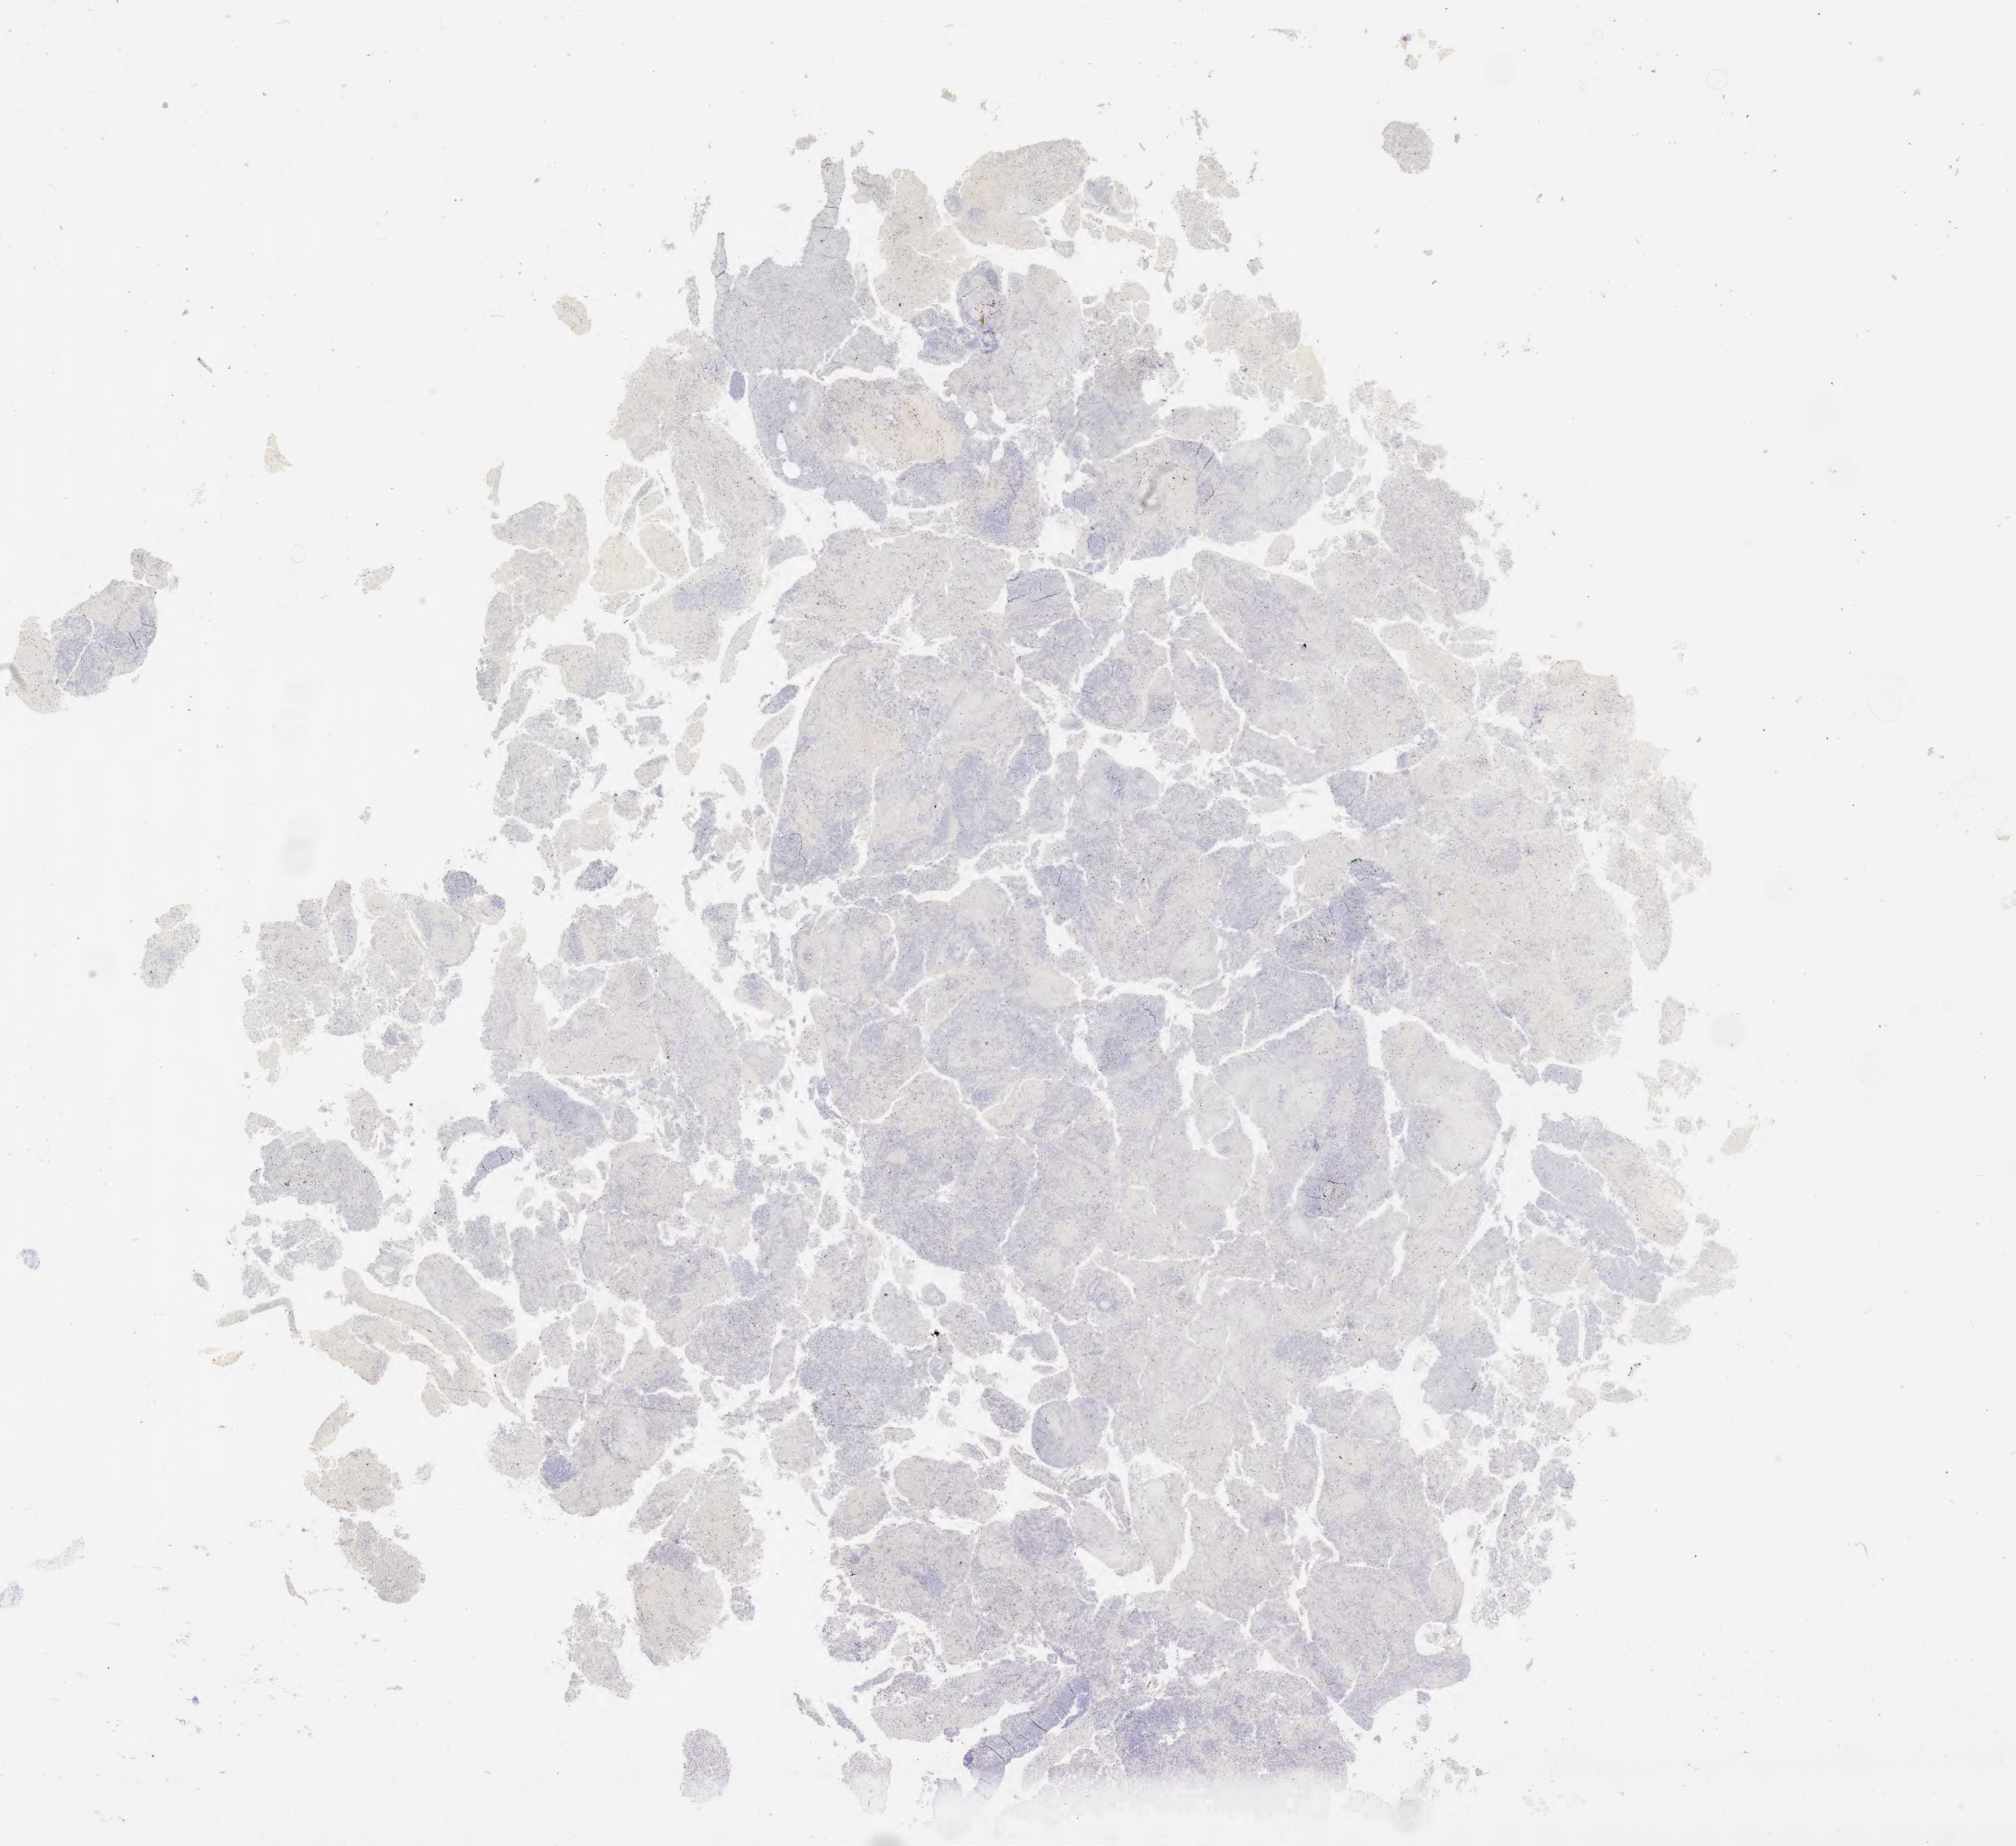
Immunohistochemistry (IHC) whole-slide image stained for CD3 — low-resolution overview of the scanned area, about 20.6 x 18.9 mm; tumor tissue; site: brain. Patient male; 51 years old.
Histologic diagnosis: Diffuse large B-cell lymphoma, NOS.